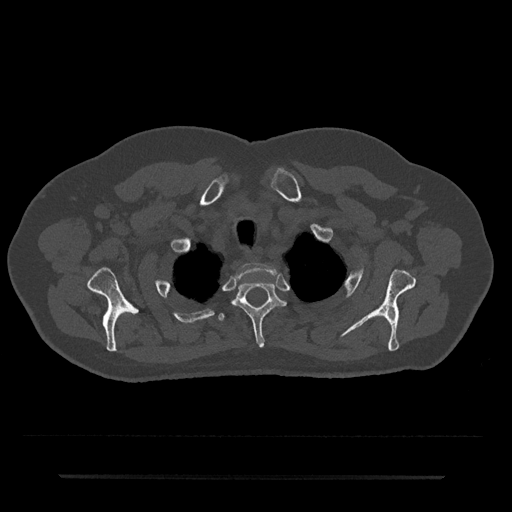
CT including the spine, one axial slice; slice 606 of 797 in the series (ordered by position); reconstruction kernel Br40s/3; 120 kVp; bone window (W 1800 / L 400 HU); 512 × 512 image matrix, field of view 437 × 437 mm. Patient: male, 69 years. From the clinical record (not read from this slice): primary cancer: prostate.
Annotated regions visible in this slice (semi-automatic segmentation, software-assisted and operator-edited):
- T1 vertebra: bounding box <236,263,278,278> (left, top, right, bottom; pixels)
- T2 vertebra: <232,281,286,347>
- T3 vertebra: <218,313,225,321>